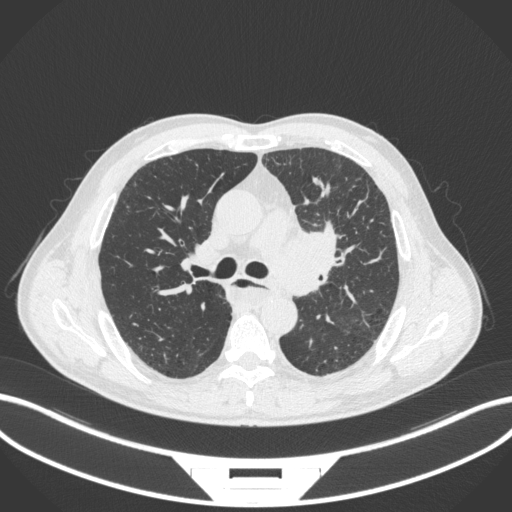
Chest CT, one axial slice. Slice 241 of 411 in the series (ordered by position). Reconstruction kernel B31f. Lung window (W 1500 / L -600 HU). 1 mm slice thickness. 512 × 512 image matrix, field of view 400 × 400 mm. Patient: male, 57 years. Case-level facts recorded for this patient, not image findings: clinical TNM (as recorded): T2a N1 M0.
Structures marked on this image (rectangle marked by the reading radiologist):
- lung tumour (recorded histology: squamous cell carcinoma): bounding box (x1, y1, x2, y2) in pixels: (264, 221, 344, 294)